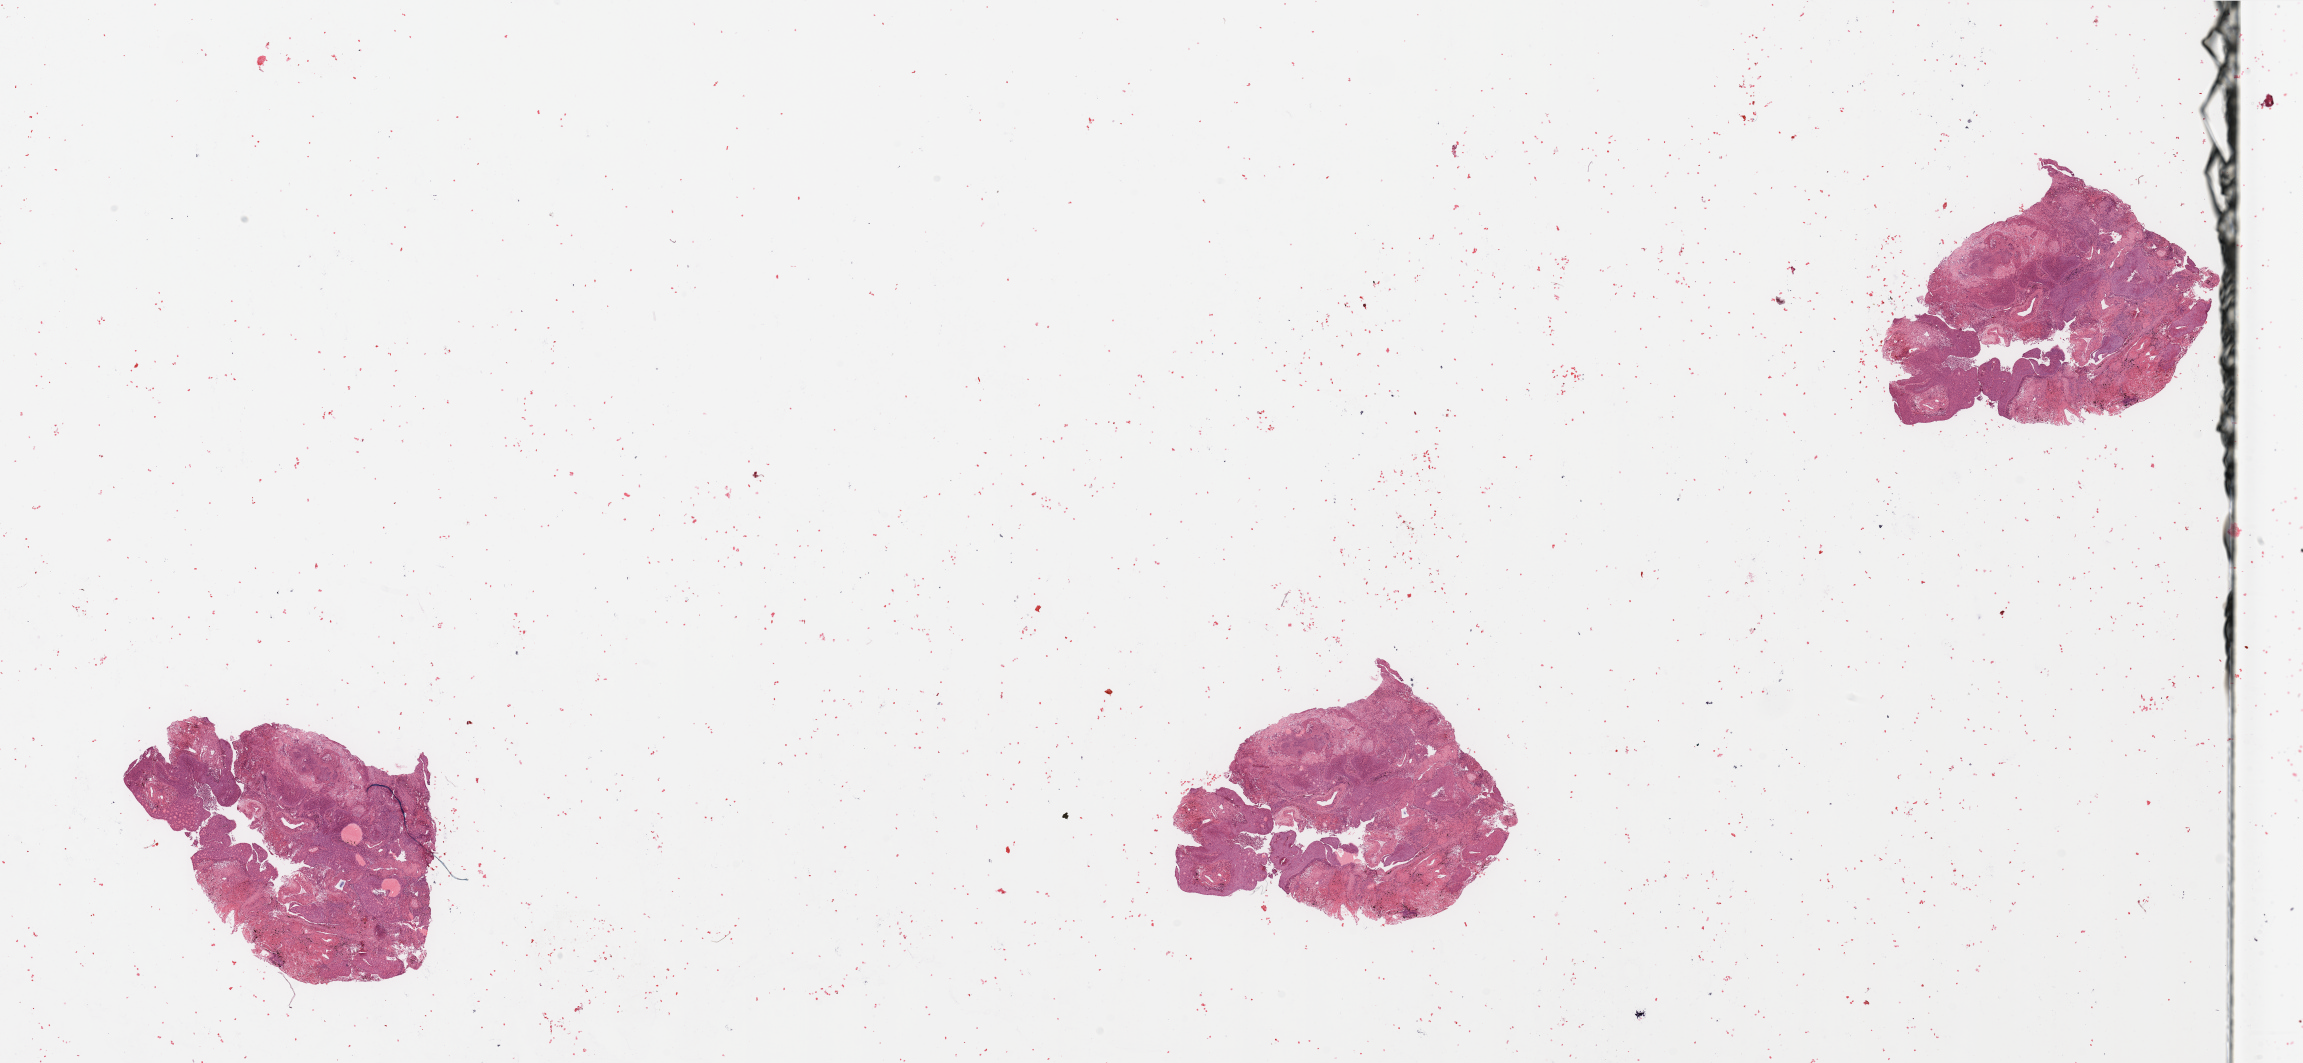
Hematoxylin and eosin (H&E) stained whole-slide image, low-resolution overview of the scanned area, about 36.4 x 16.8 mm. Lung, tumour tissue. 72-year-old female patient. Histologic grade: G2 (moderately differentiated).
• diagnosis: Squamous cell carcinoma, NOS
• AJCC pathologic stage: IIB
• primary tumour site (as recorded): left lower lobe